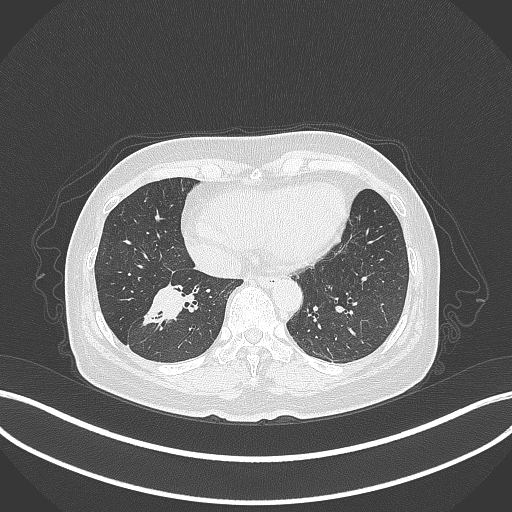
Chest CT, one axial slice. Slice 126 of 429 in the series (ordered by position). Reconstruction kernel B70f. 120 kVp. Lung window (W 1500 / L -600 HU). 1 mm slice thickness. 512 × 512 image matrix, field of view 400 × 400 mm. Female patient, age 67 years. From the clinical record (not read from this slice): clinical TNM (as recorded): T1c N1 M0.
Structures marked on this image (rectangle marked by the reading radiologist):
- lung tumour (recorded histology: adenocarcinoma): bounding box <141,280,187,329> (left, top, right, bottom; pixels)